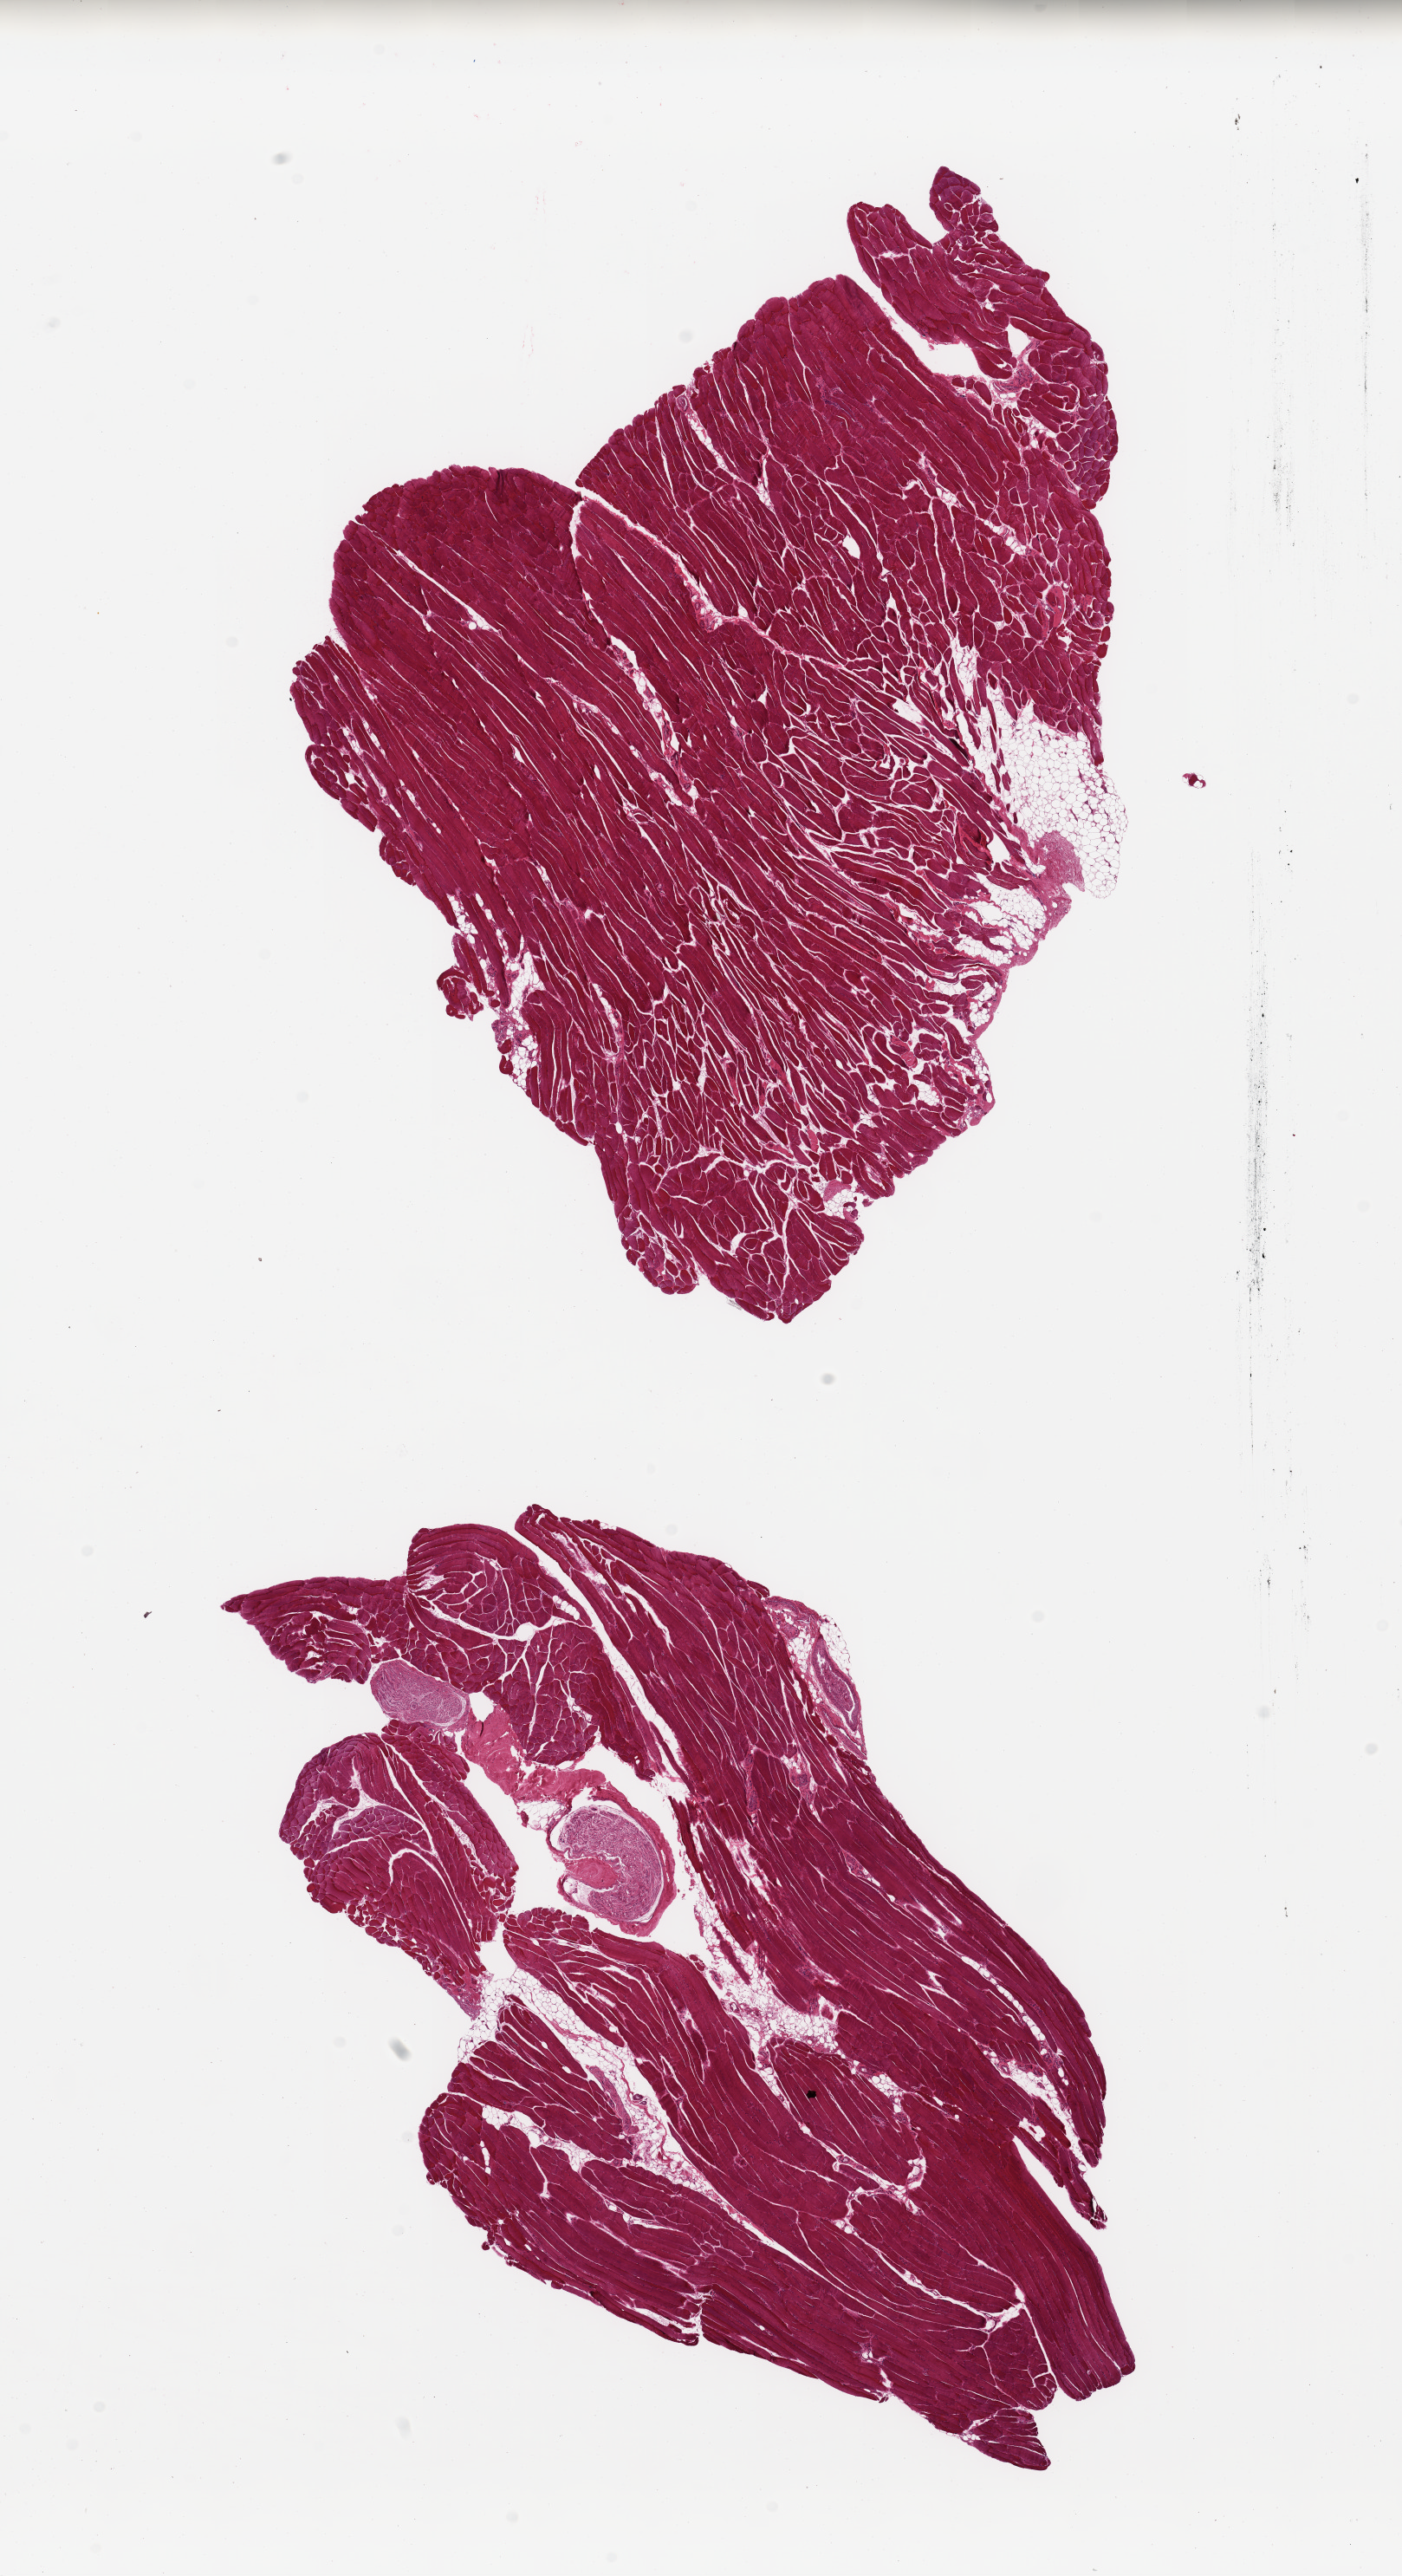
Digitized H&E-stained section — whole scanned area (about 12.8 x 23.5 mm, from a 20x scan) shown as a low-resolution overview, PAXgene-fixed, paraffin-embedded tissue, target tissue: skeletal muscle, donor tissue sample. Donor sex: male.
Review note (as recorded): 2 pieces; skeletal muscle with small portion of fat, one contains nerves.